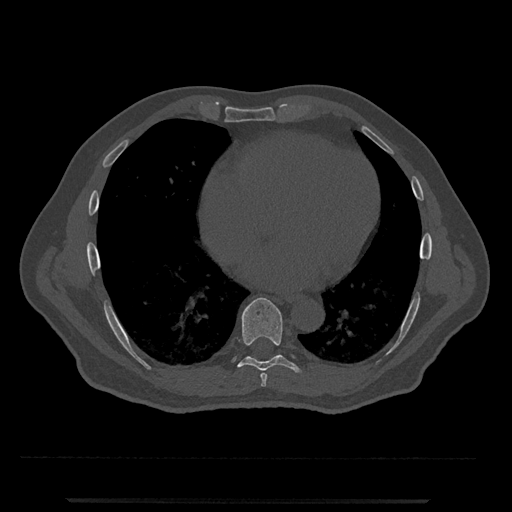
CT including the spine, one axial slice. Slice 626 of 797 in the series (ordered by position). Reconstruction kernel Br40s/3. 120 kVp. Bone window (W 1800 / L 400 HU). 0.5 mm slice thickness. 512 × 512 image matrix, field of view 419 × 419 mm. Male patient, age 63 years. From the clinical record (not read from this slice): primary cancer: prostate.
Outlined on this slice (semi-automatically segmented with operator editing):
- T7 vertebra: bounding box [x1, y1, x2, y2] px = [260, 373, 267, 387]
- T8 vertebra: [232, 298, 300, 372]